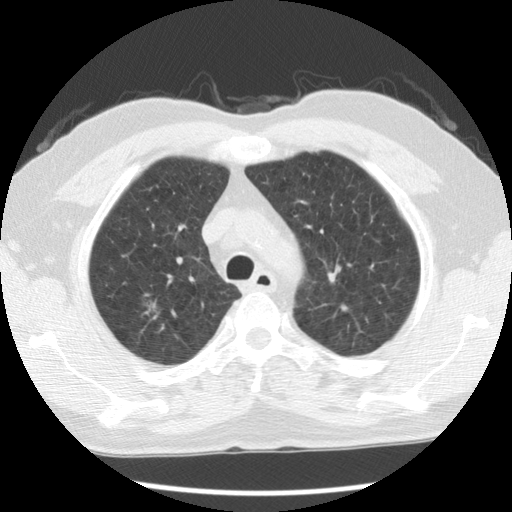
Axial slice from a low-dose chest CT screening exam, first (baseline) screen, lung window (W 1500 / L -600 HU), 2.5 mm slice thickness, slice 86 of 110 in the series. Male participant, aged 68 years at enrolment. Former smoker at enrolment.
Lesion marked by an expert reader, box from (x=133, y=292) to (x=169, y=327) px. Screening reader's record for this exam (one nodule recorded; not confirmed to be the boxed lesion): non-calcified nodule or mass ≥4 mm, right upper lobe, 9 × 7 mm, poorly defined margins, ground glass attenuation.